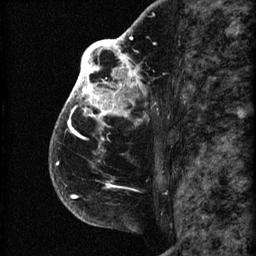
Breast MRI (dynamic contrast-enhanced), one sagittal slice; position 45 of 60 along the scan axis; 3 images stored at this slice position (order not interpretable as contrast timing); 1.5 T; TE 4.2 ms, TR 22.7 ms; 2 mm slice thickness; 256 × 256 image matrix, field of view 180 × 180 mm. Patient: female, 48 years. Case-level facts recorded for this patient, not image findings: setting: breast cancer imaged before/during neoadjuvant chemotherapy; receptor status: triple-negative.
Outlined on this slice (semi-automatic segmentation, software-assisted and operator-edited):
- analysis volume of interest (the breast-tissue region the enhancement analysis was run in; not a lesion): bounding box [x1, y1, x2, y2] px = [49, 30, 173, 207]
- tumour enhancement mask (voxels above the 90 % enhancement threshold inside the analysis volume of interest): [54, 30, 144, 198]